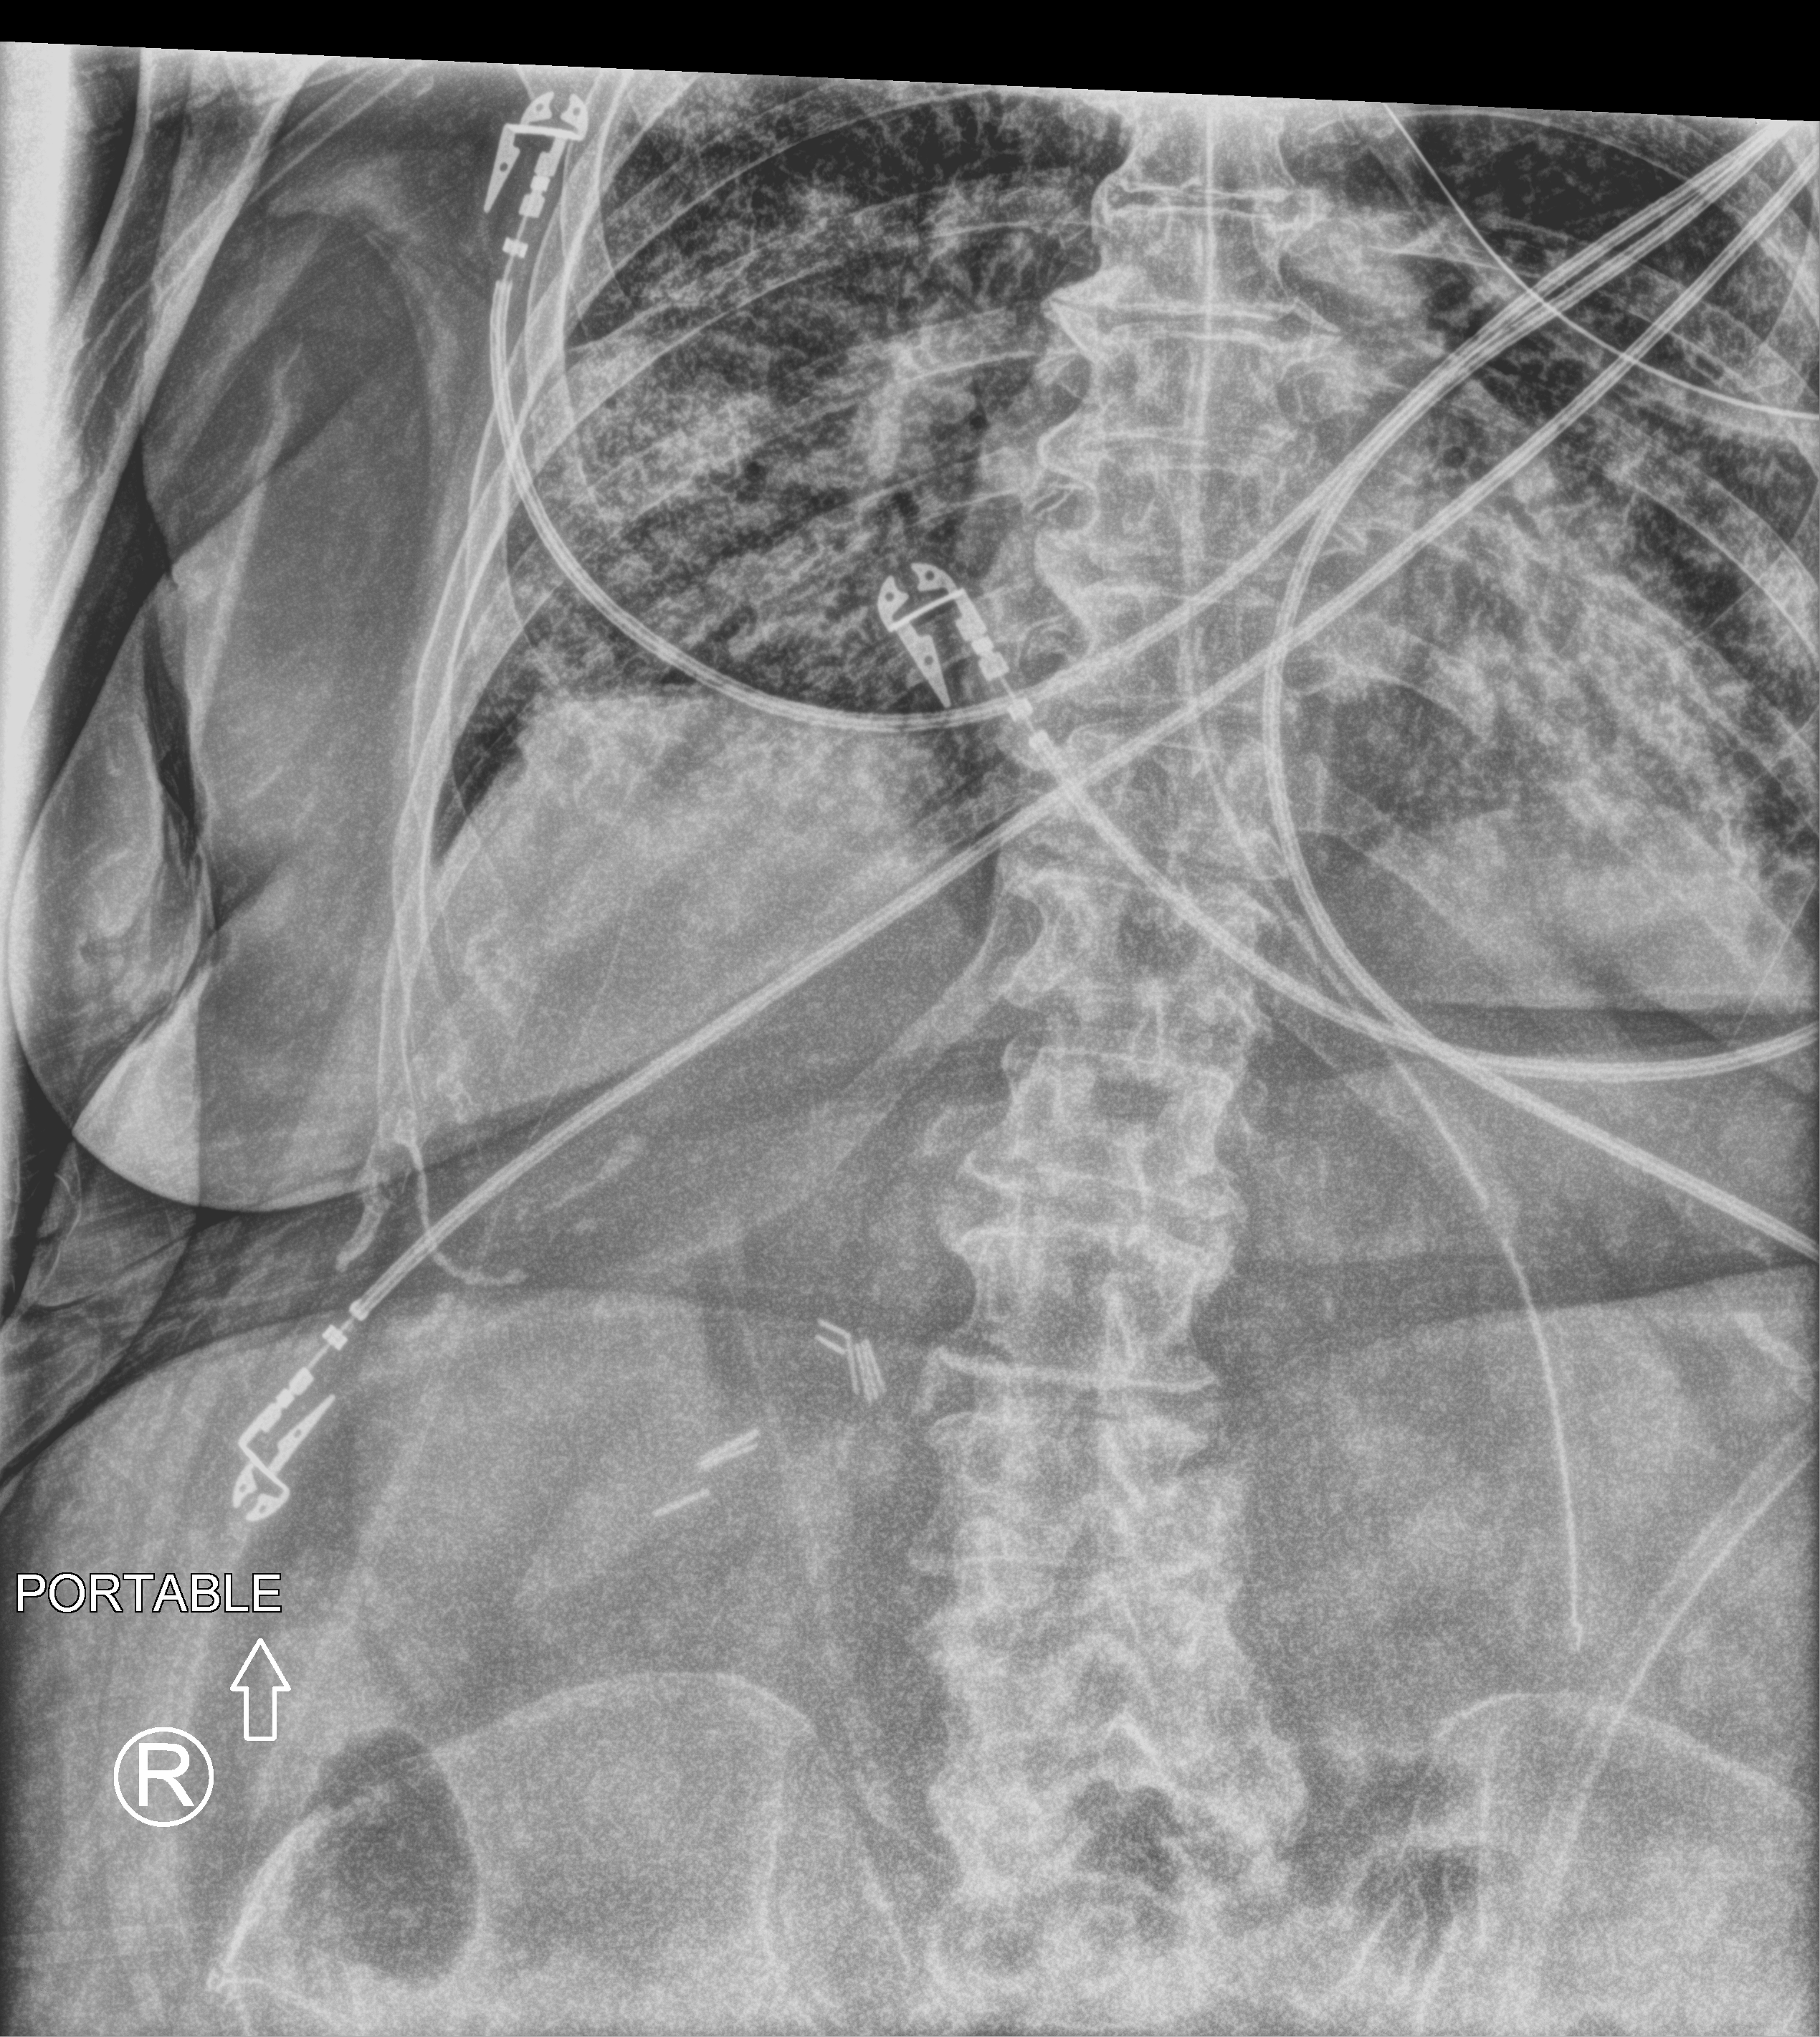
Portable abdomen radiograph. Female patient hospitalised with COVID-19, age 75–90 years.
Admission-level facts for this patient (not findings on this image; timing relative to this image not recorded): other chronic lung disease (admission record): no; admitted to intensive care during this hospital stay: no; mechanically ventilated during this hospital stay: yes.